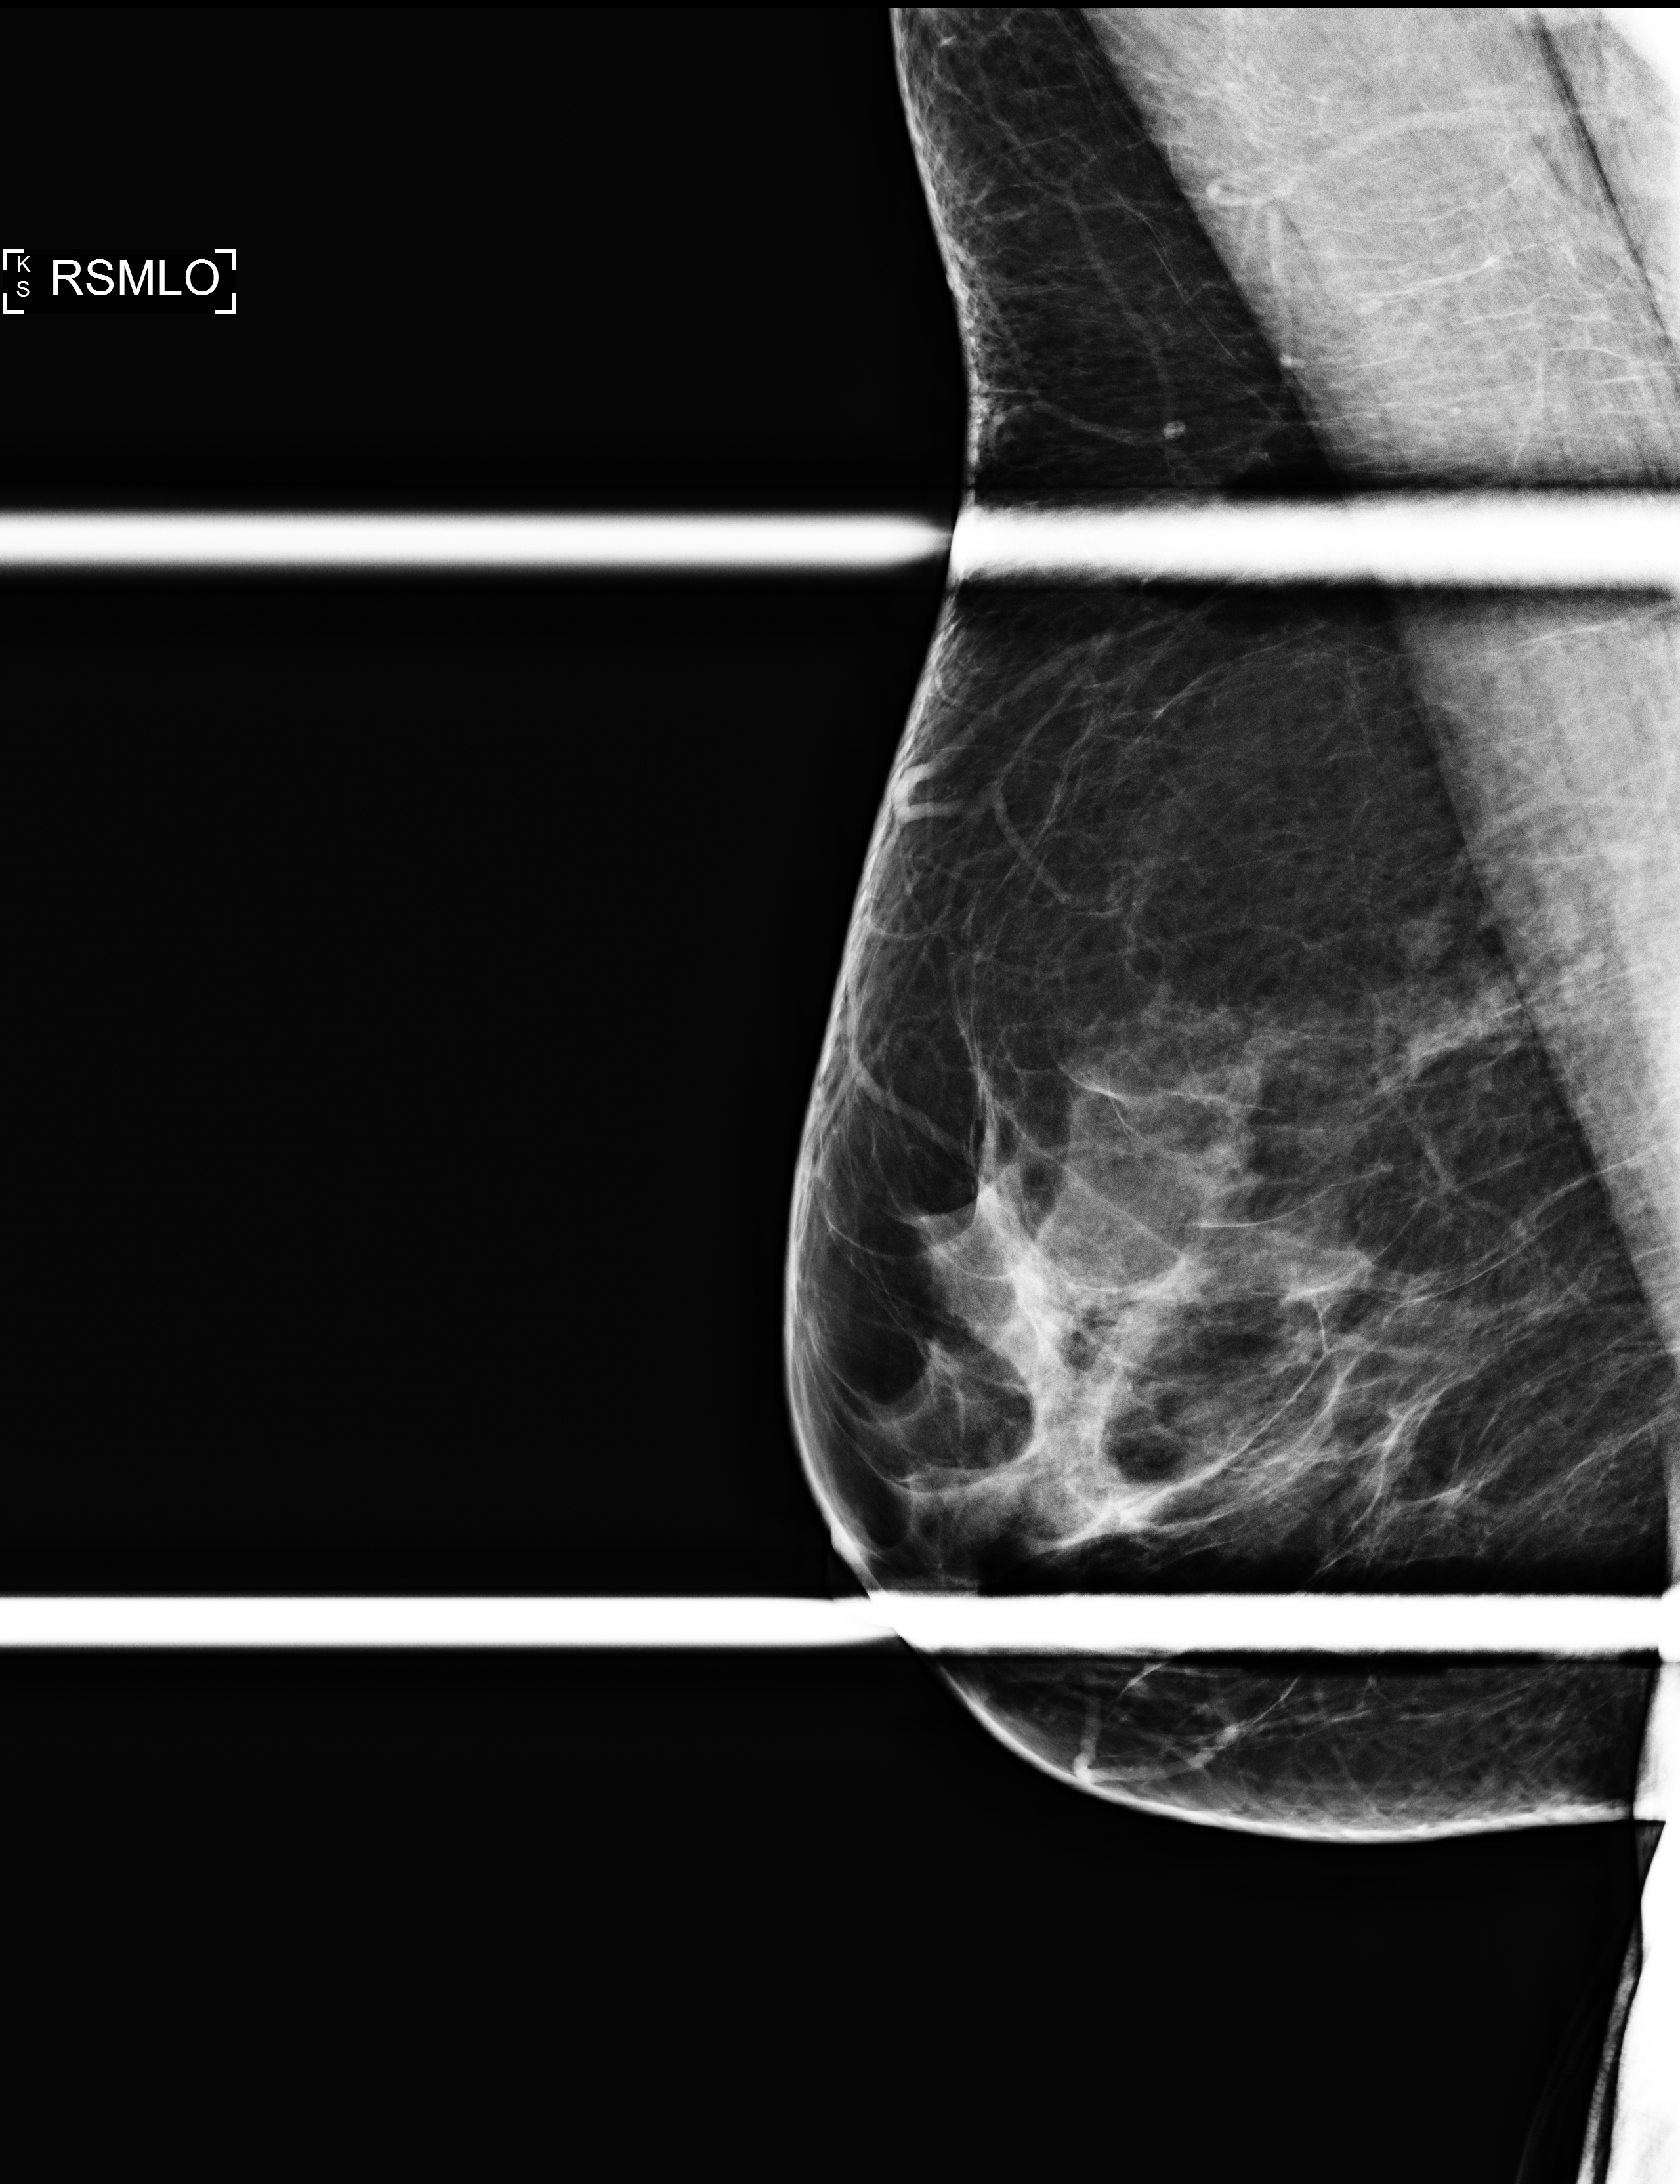
Full-field digital mammogram (FFDM), right breast, MLO view (spot compression), additional work-up view. Patient: female, 49 years.
- BI-RADS breast density category at the screening exam (both breasts, scale 1–4): 3
- final BI-RADS assessment for this screening round (tomosynthesis exam, both breasts): category 2
- recall: recalled for additional imaging after this screen